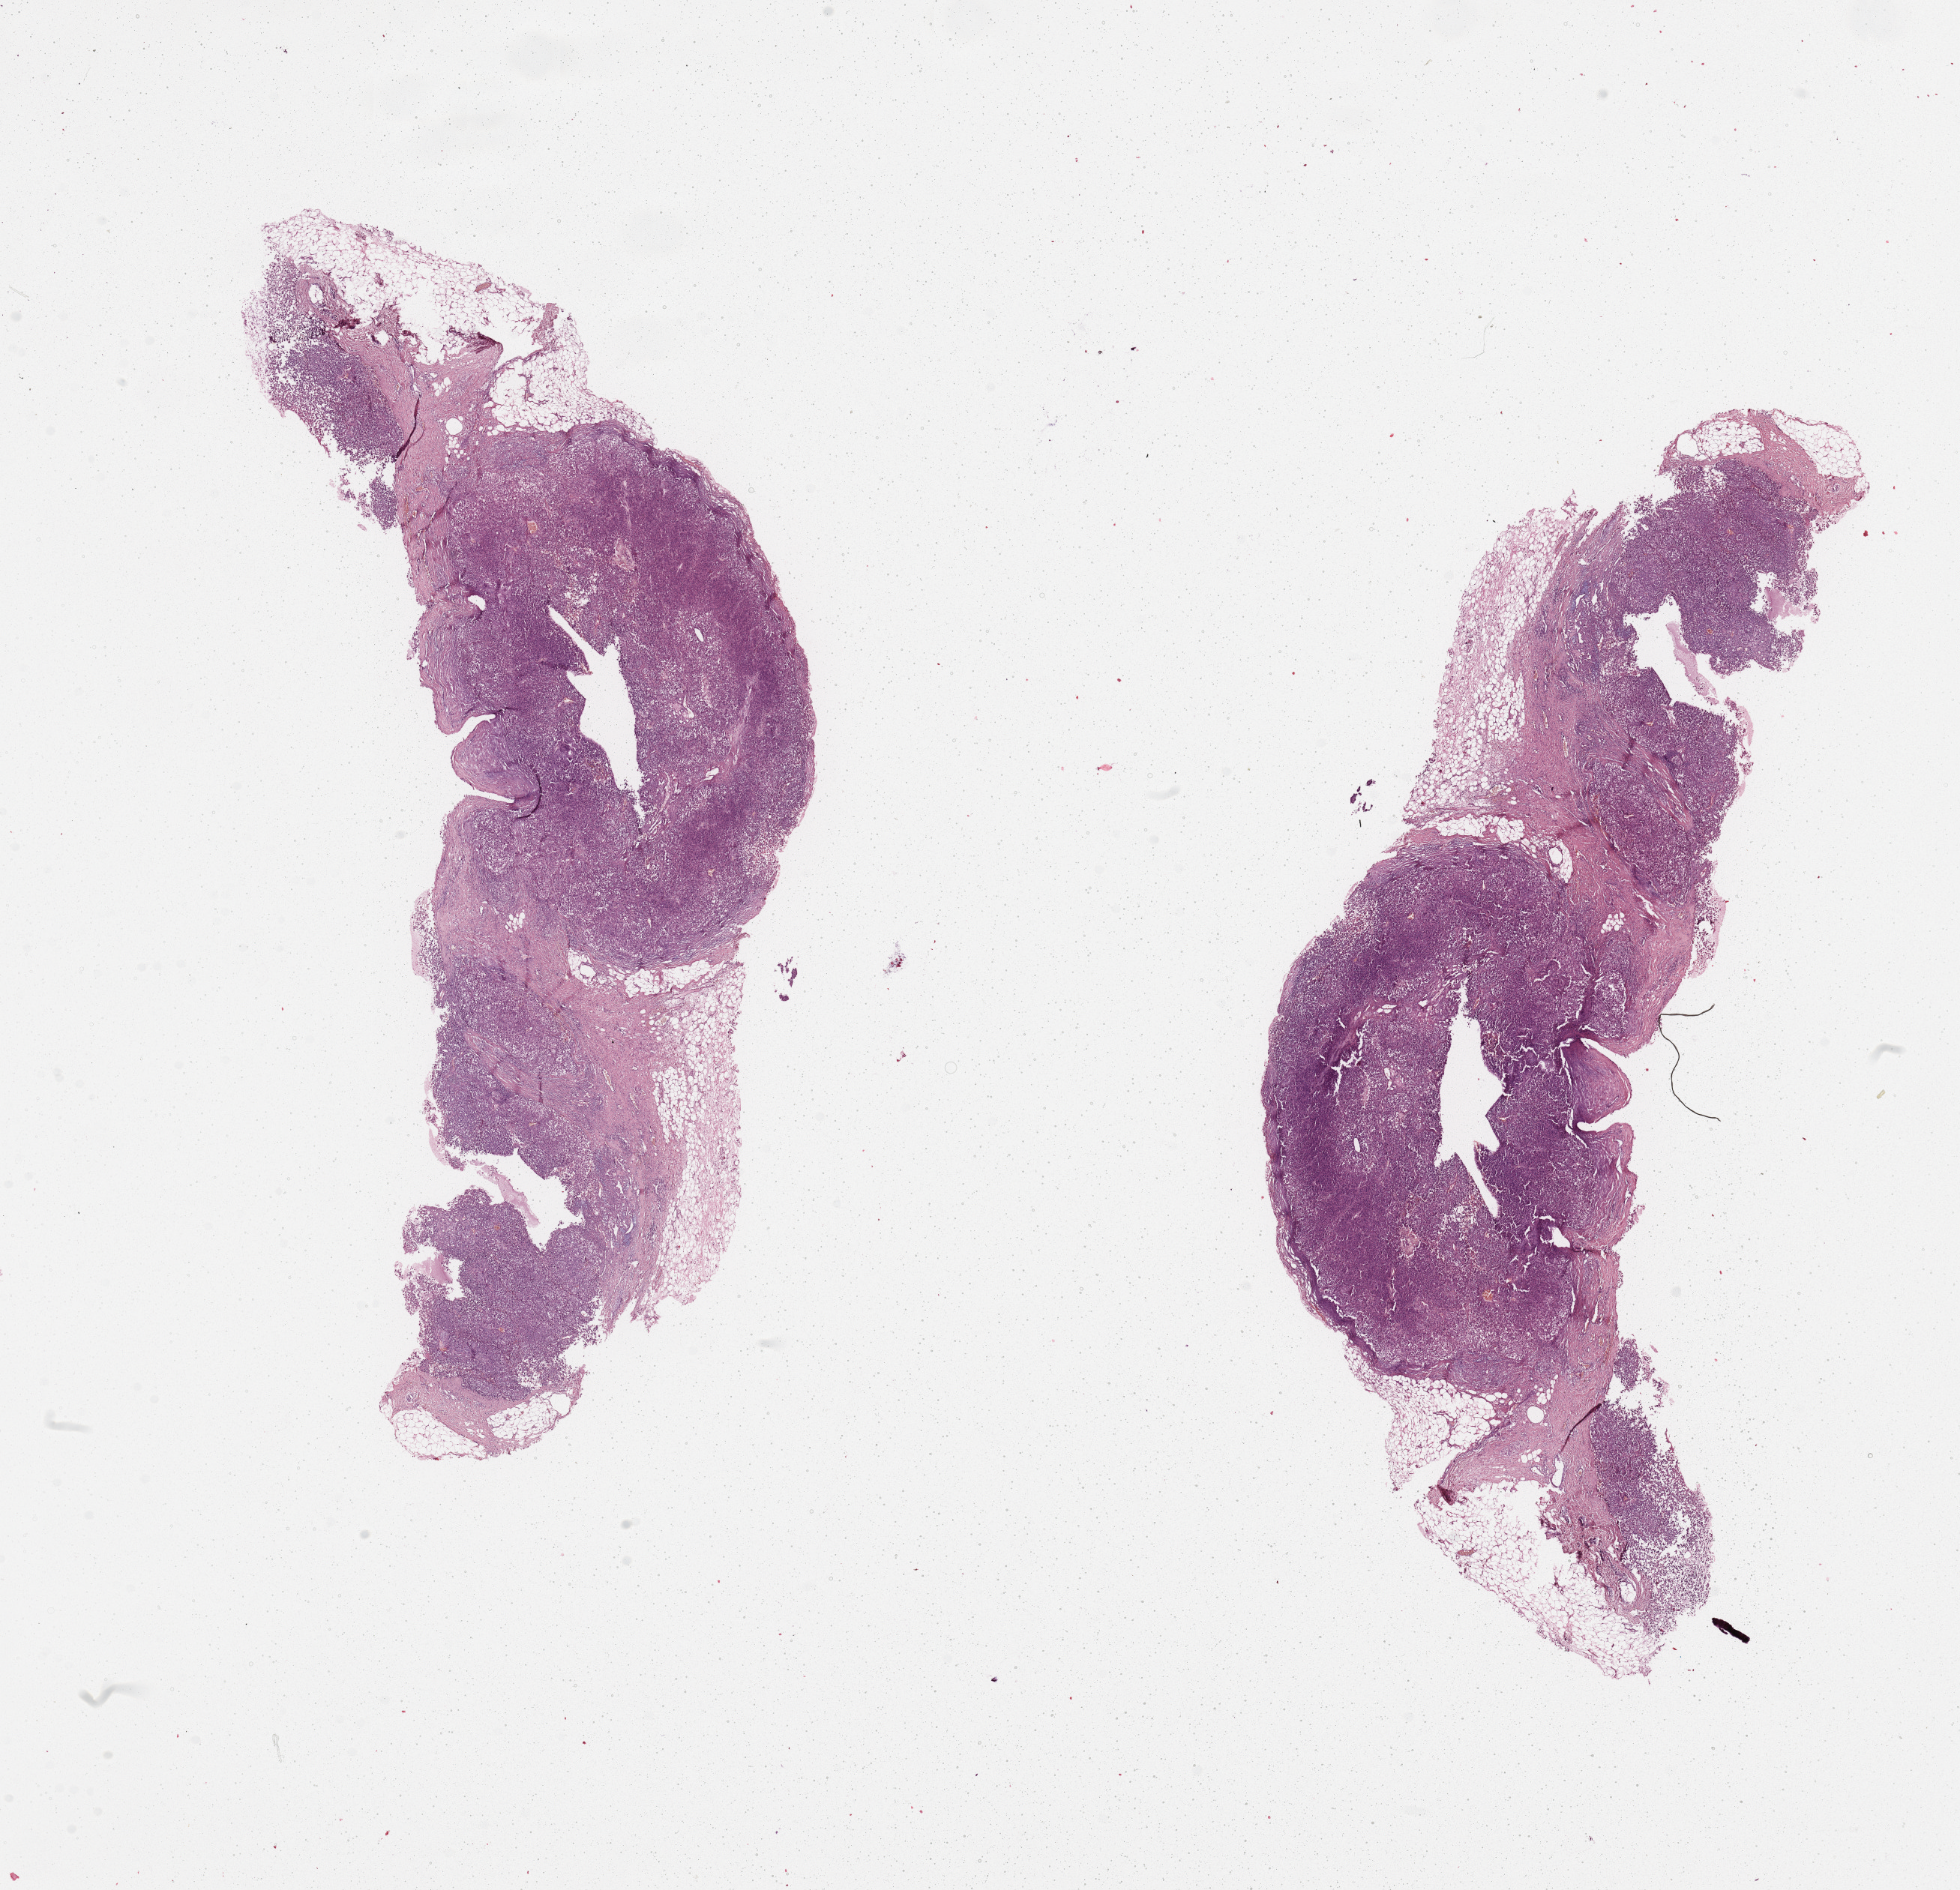
H&E-stained whole-slide image, shown as a low-resolution overview of the whole scanned area (about 20.7 x 19.9 mm, acquisition: 20x scan); melanoma tumour tissue; sampled site not recorded. Patient: female, age 45 years.
AJCC pathologic stage: IIA. Diagnosis: Malignant melanoma, NOS.